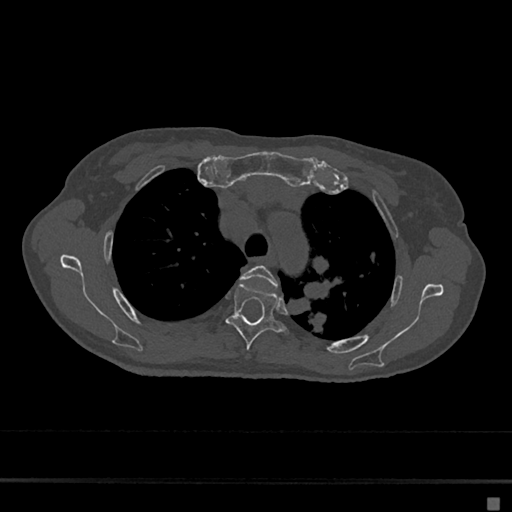
CT including the spine, one axial slice; slice 505 of 797 in the series (ordered by position); reconstruction kernel Br40s/3; 120 kVp; bone window (W 1800 / L 400 HU); 0.5 mm slice thickness; 512 × 512 image matrix, field of view 360 × 360 mm. Female patient, age 68 years. From the clinical record (not read from this slice): primary cancer: renal.
Outlined on this slice (semi-automatically segmented with operator editing):
- T3 vertebra: bounding box <240,265,277,287> (left, top, right, bottom; pixels)
- T4 vertebra: <226,283,288,349>